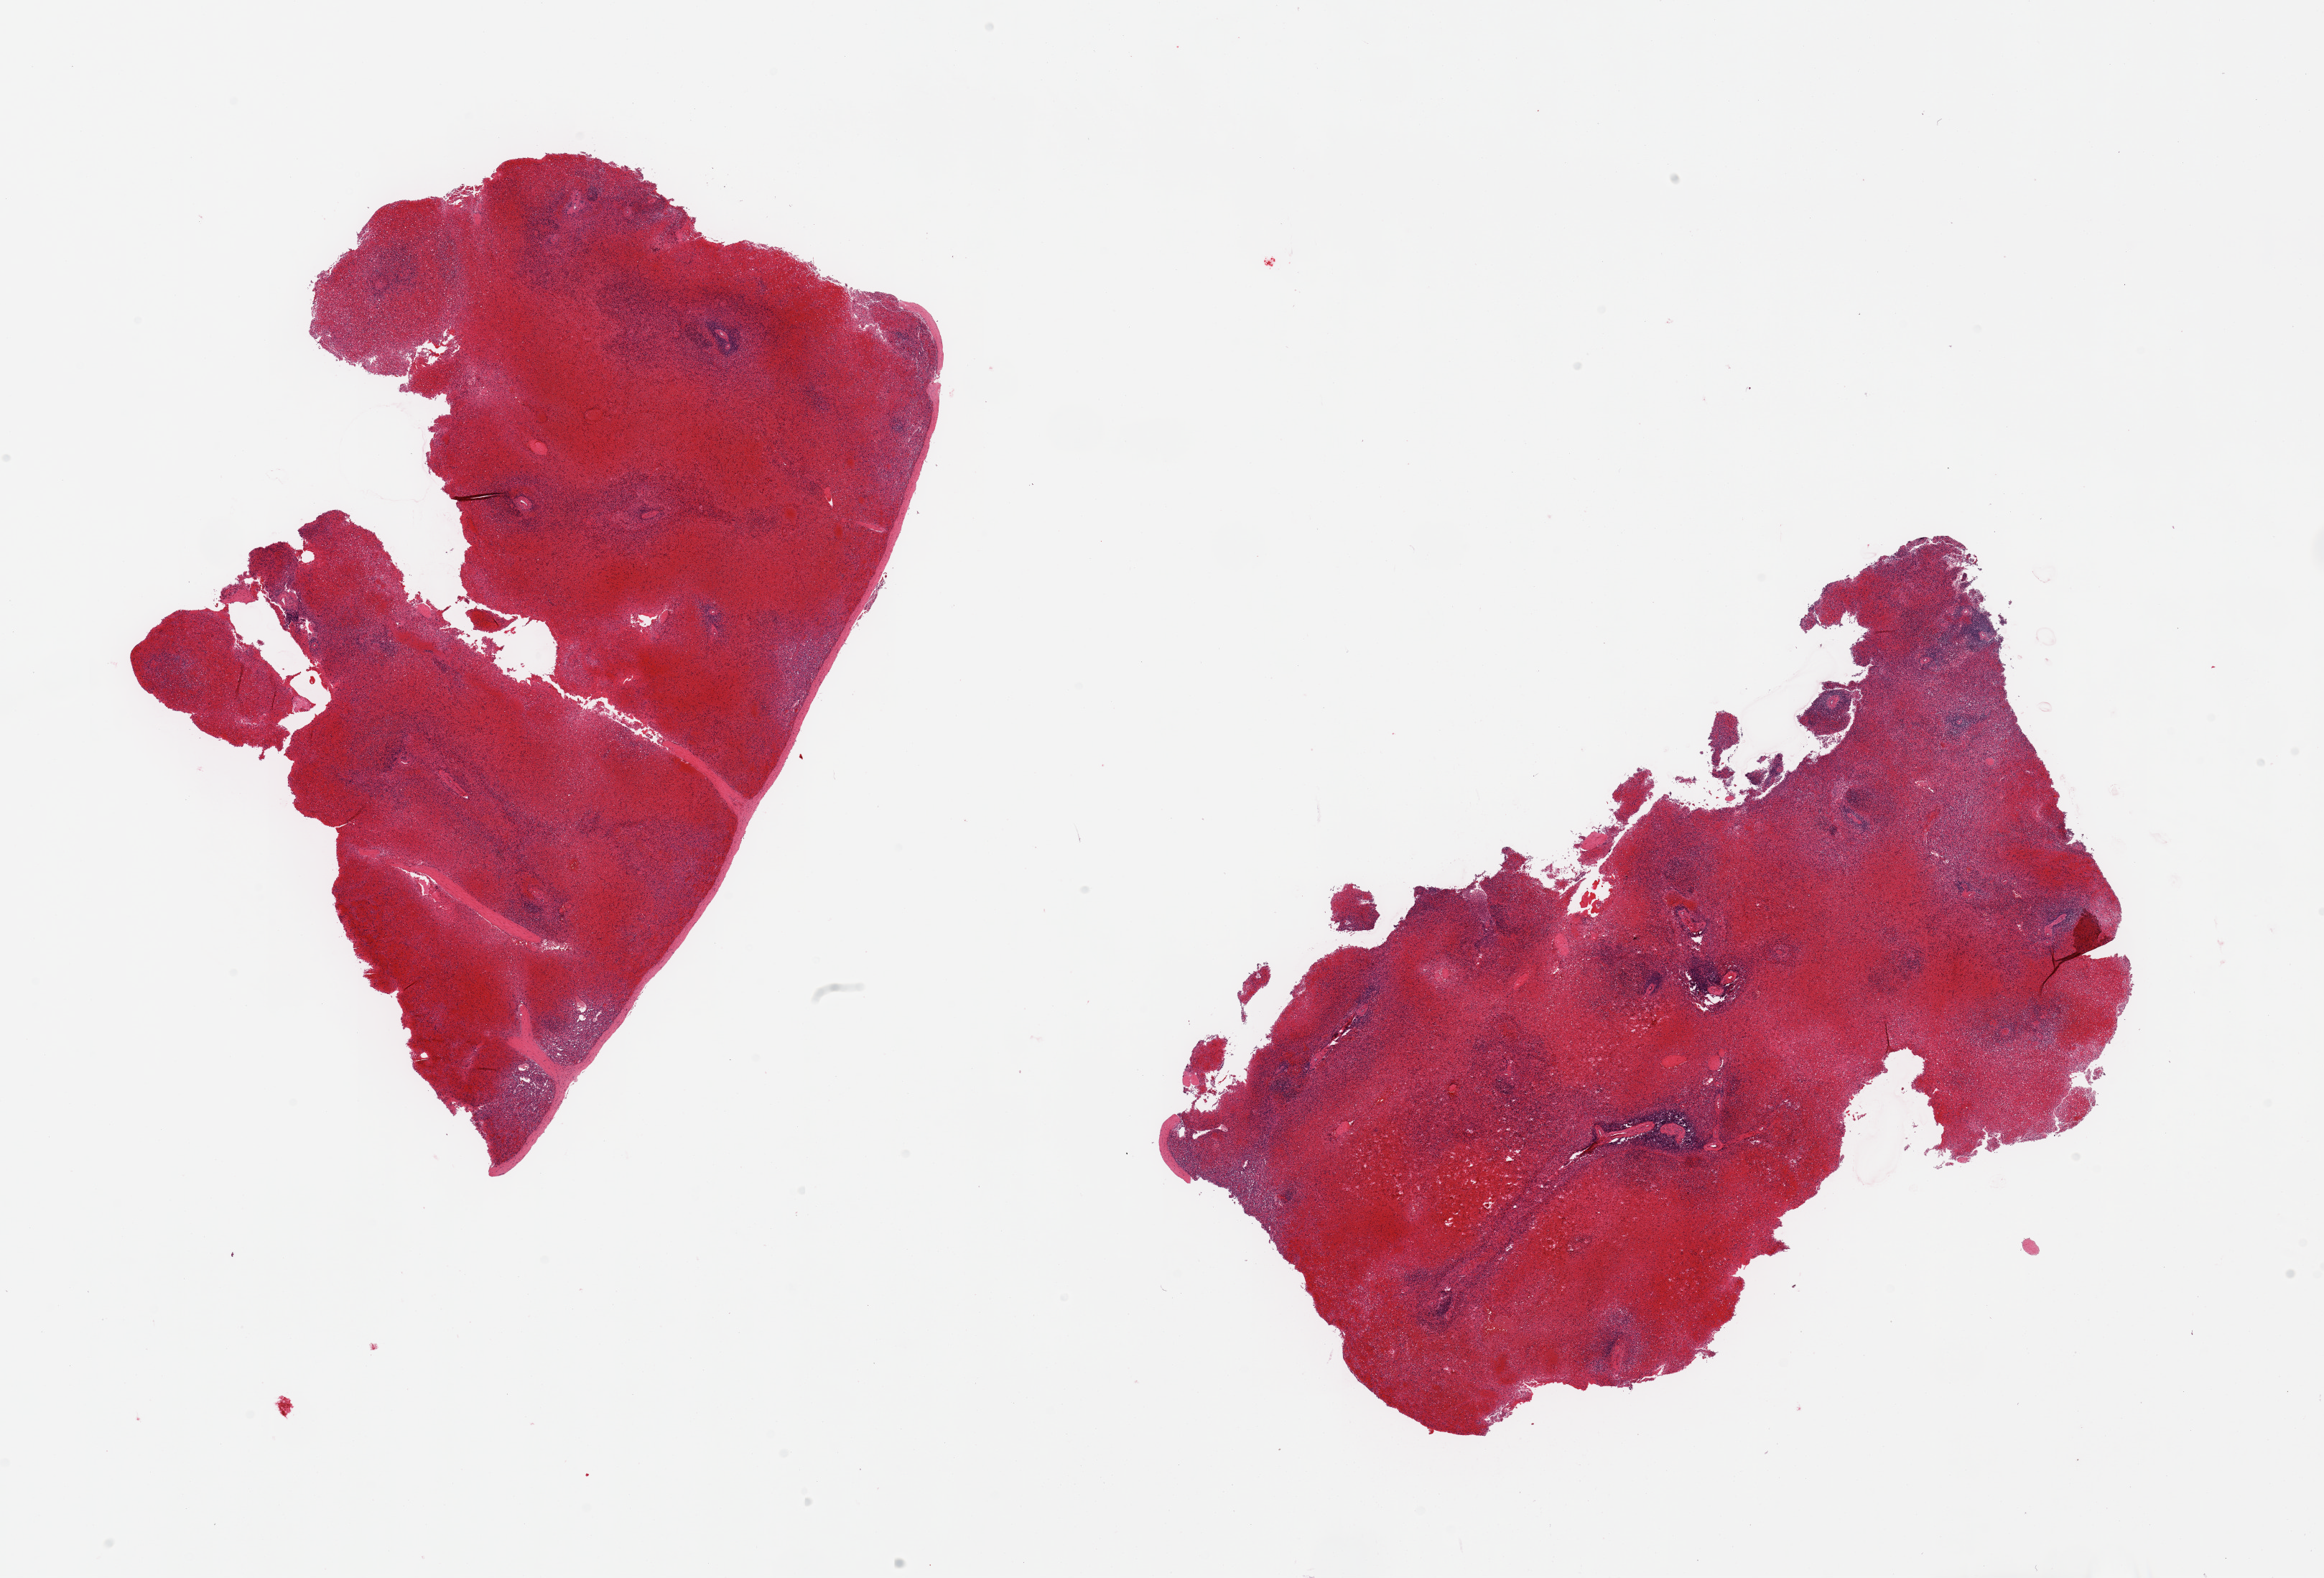
Whole-slide image, hematoxylin and eosin (H&E) stain, brightfield, low-resolution overview of the scanned area, about 25.6 x 17.4 mm, PAXgene-fixed, paraffin-embedded tissue, section of spleen (target tissue), donor tissue sample. Donor: male.
- pathologist's review note for this sample: 2 pieces; congestion/hemorrhage, includes capsule (target is 5mm below capsule)